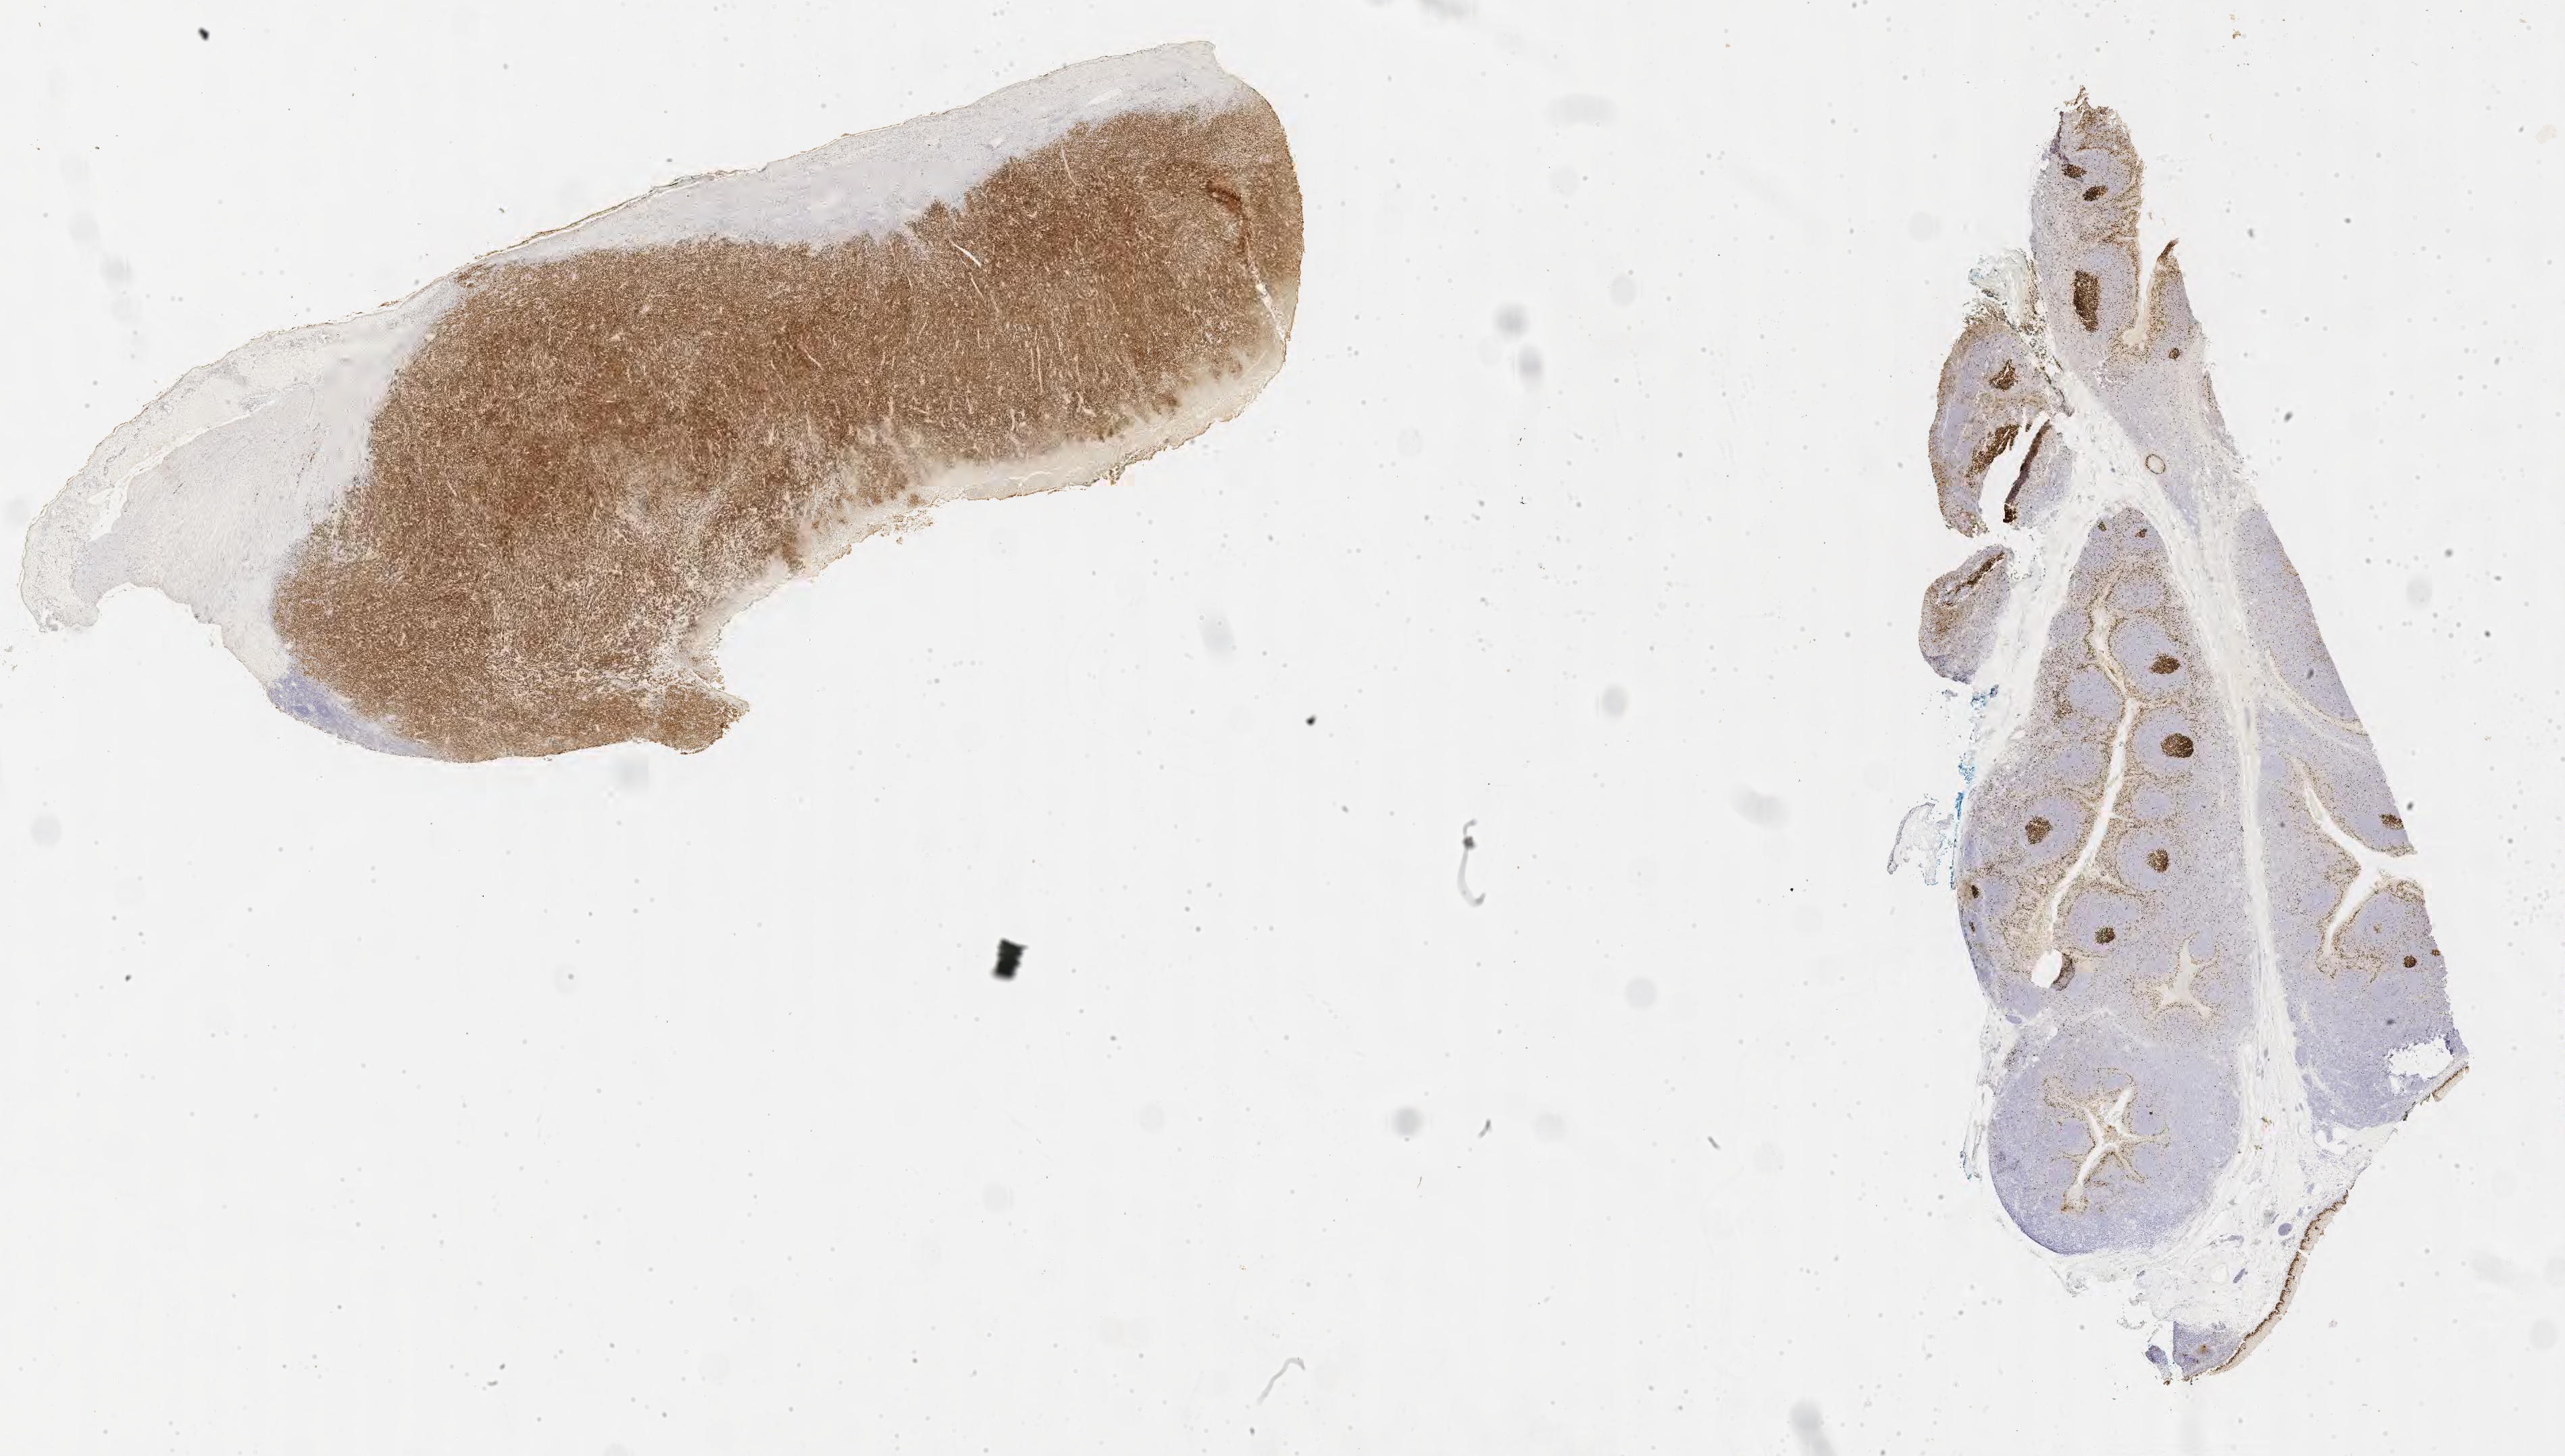
Whole-slide image, immunohistochemical stain for Ki-67 — low-resolution overview of the scanned area, about 30.7 x 17.4 mm. Tumor tissue. Anatomic site: small intestine. Patient: male, age at initial diagnosis 3 years.
Histologic diagnosis: Burkitt lymphoma, NOS.